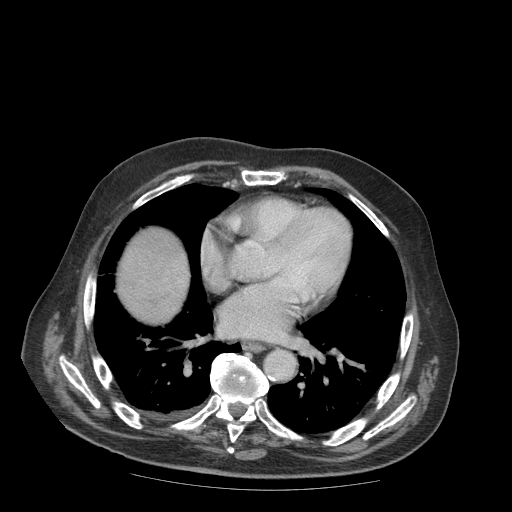
Contrast-enhanced abdominal CT (liver protocol), one axial slice. Slice 94 of 99 in the series (ordered by position). Reconstruction kernel STANDARD. 140 kVp. Soft-tissue window (W 400 / L 40 HU). 2.5 mm slice thickness. 512 × 512 image matrix, field of view 420 × 420 mm. From the clinical record (not read from this slice): diagnosis: hepatocellular carcinoma (patient treated with transarterial chemoembolisation; whether this scan precedes or follows treatment is not stated here); TNM stage (as recorded): Stage-IIIB; Child-Pugh class: A; tumour nodularity: multinodular.
Structures marked on this image (semi-automatic segmentation, software-assisted and operator-edited):
- liver parenchyma outside the tumour (the mass and vessels are separate outlines, so this box may not span the whole liver): box from (x=118, y=228) to (x=190, y=322) px